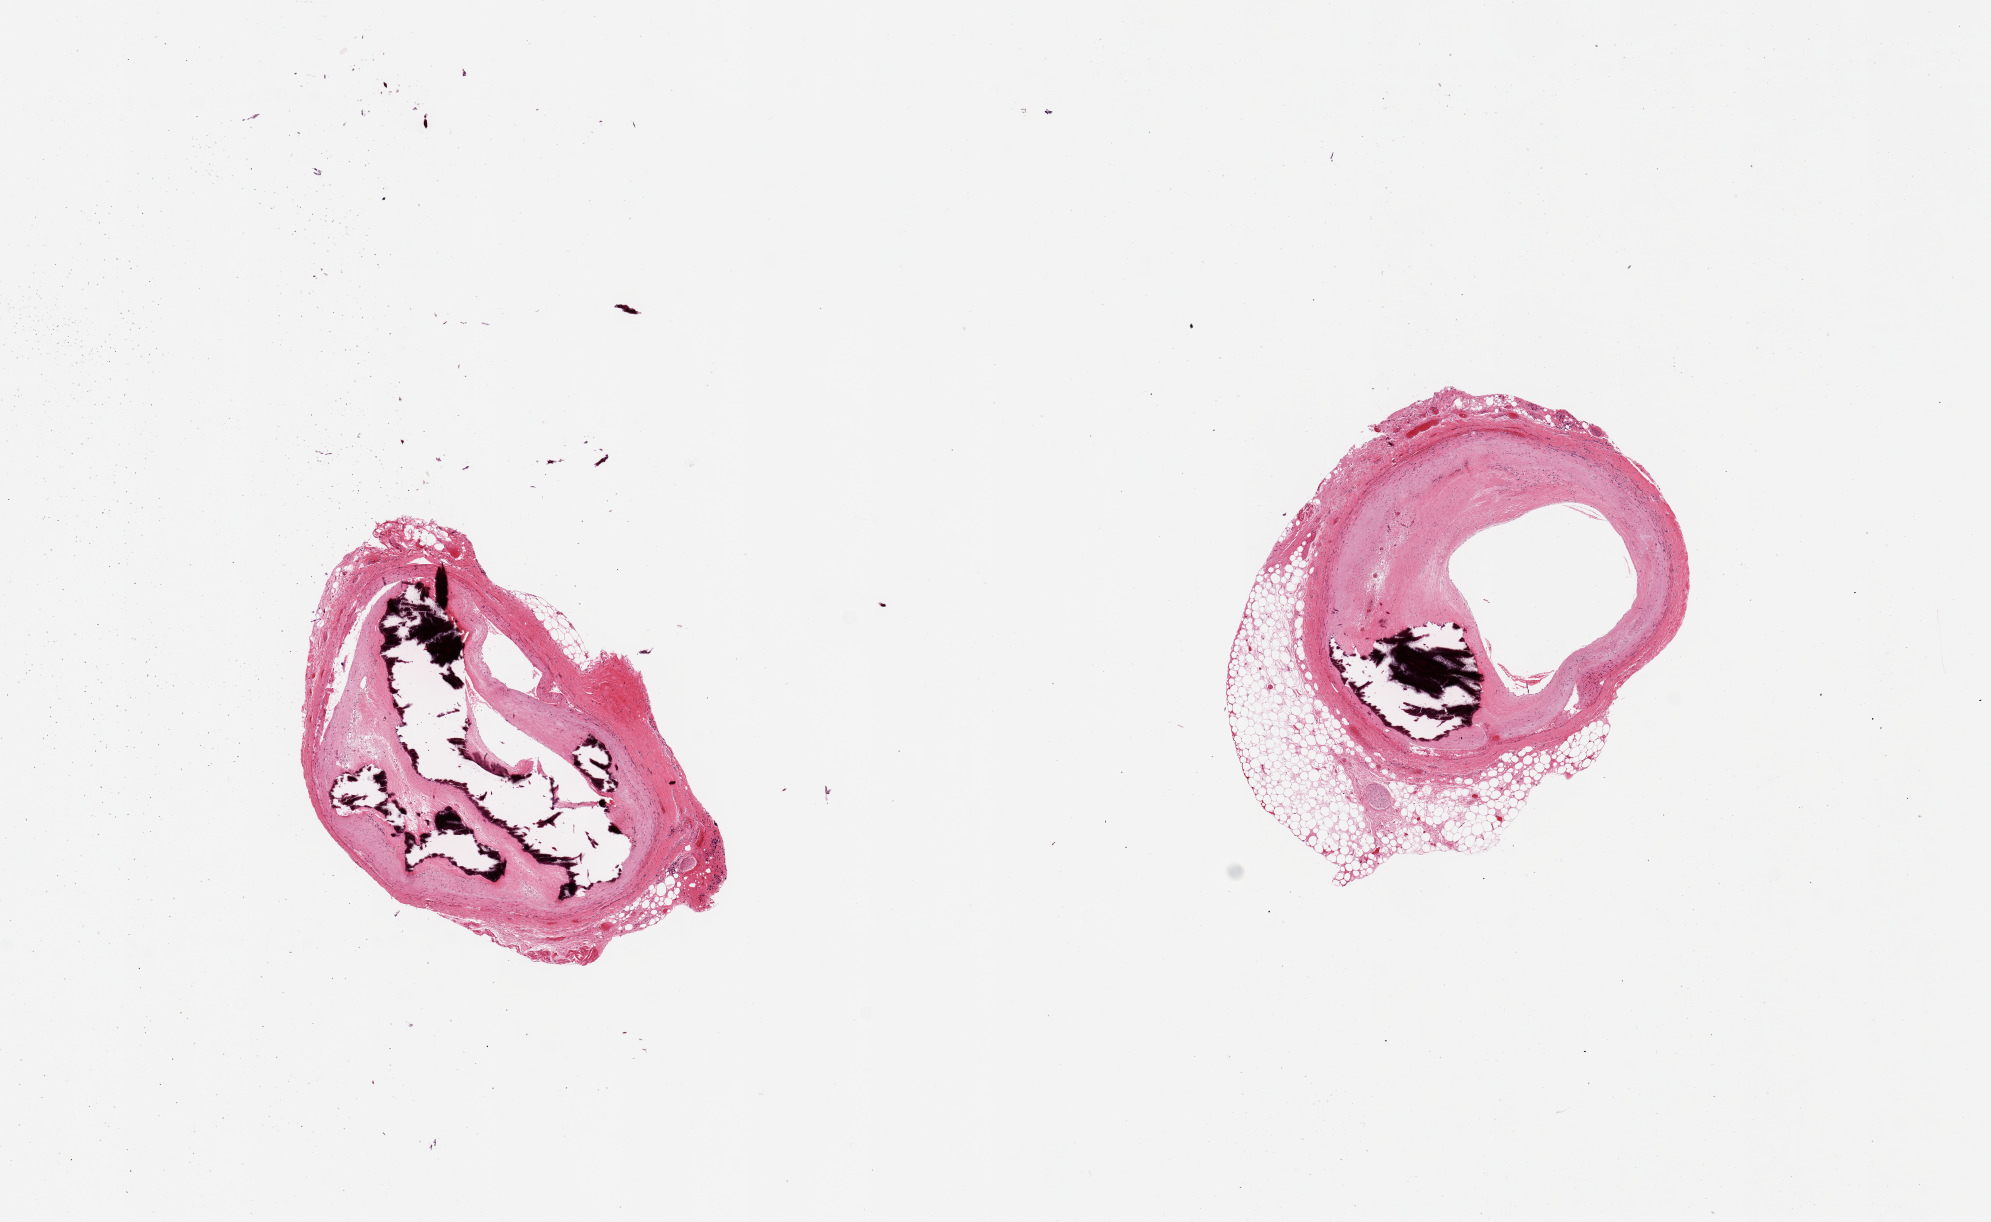
Whole-slide image, H&E stain, brightfield, whole scanned area (about 15.8 x 9.7 mm, acquisition: 20x scan) shown as a low-resolution overview. PAXgene-fixed, paraffin-embedded tissue. Section of coronary artery (target tissue). Donor tissue sample. Donor: female.
- reviewer comment on this tissue sample: 2 pieces, calicifying atherosclerotic deposits, 60% to subtotally occlusive; rim of fat on one ~0.6mm